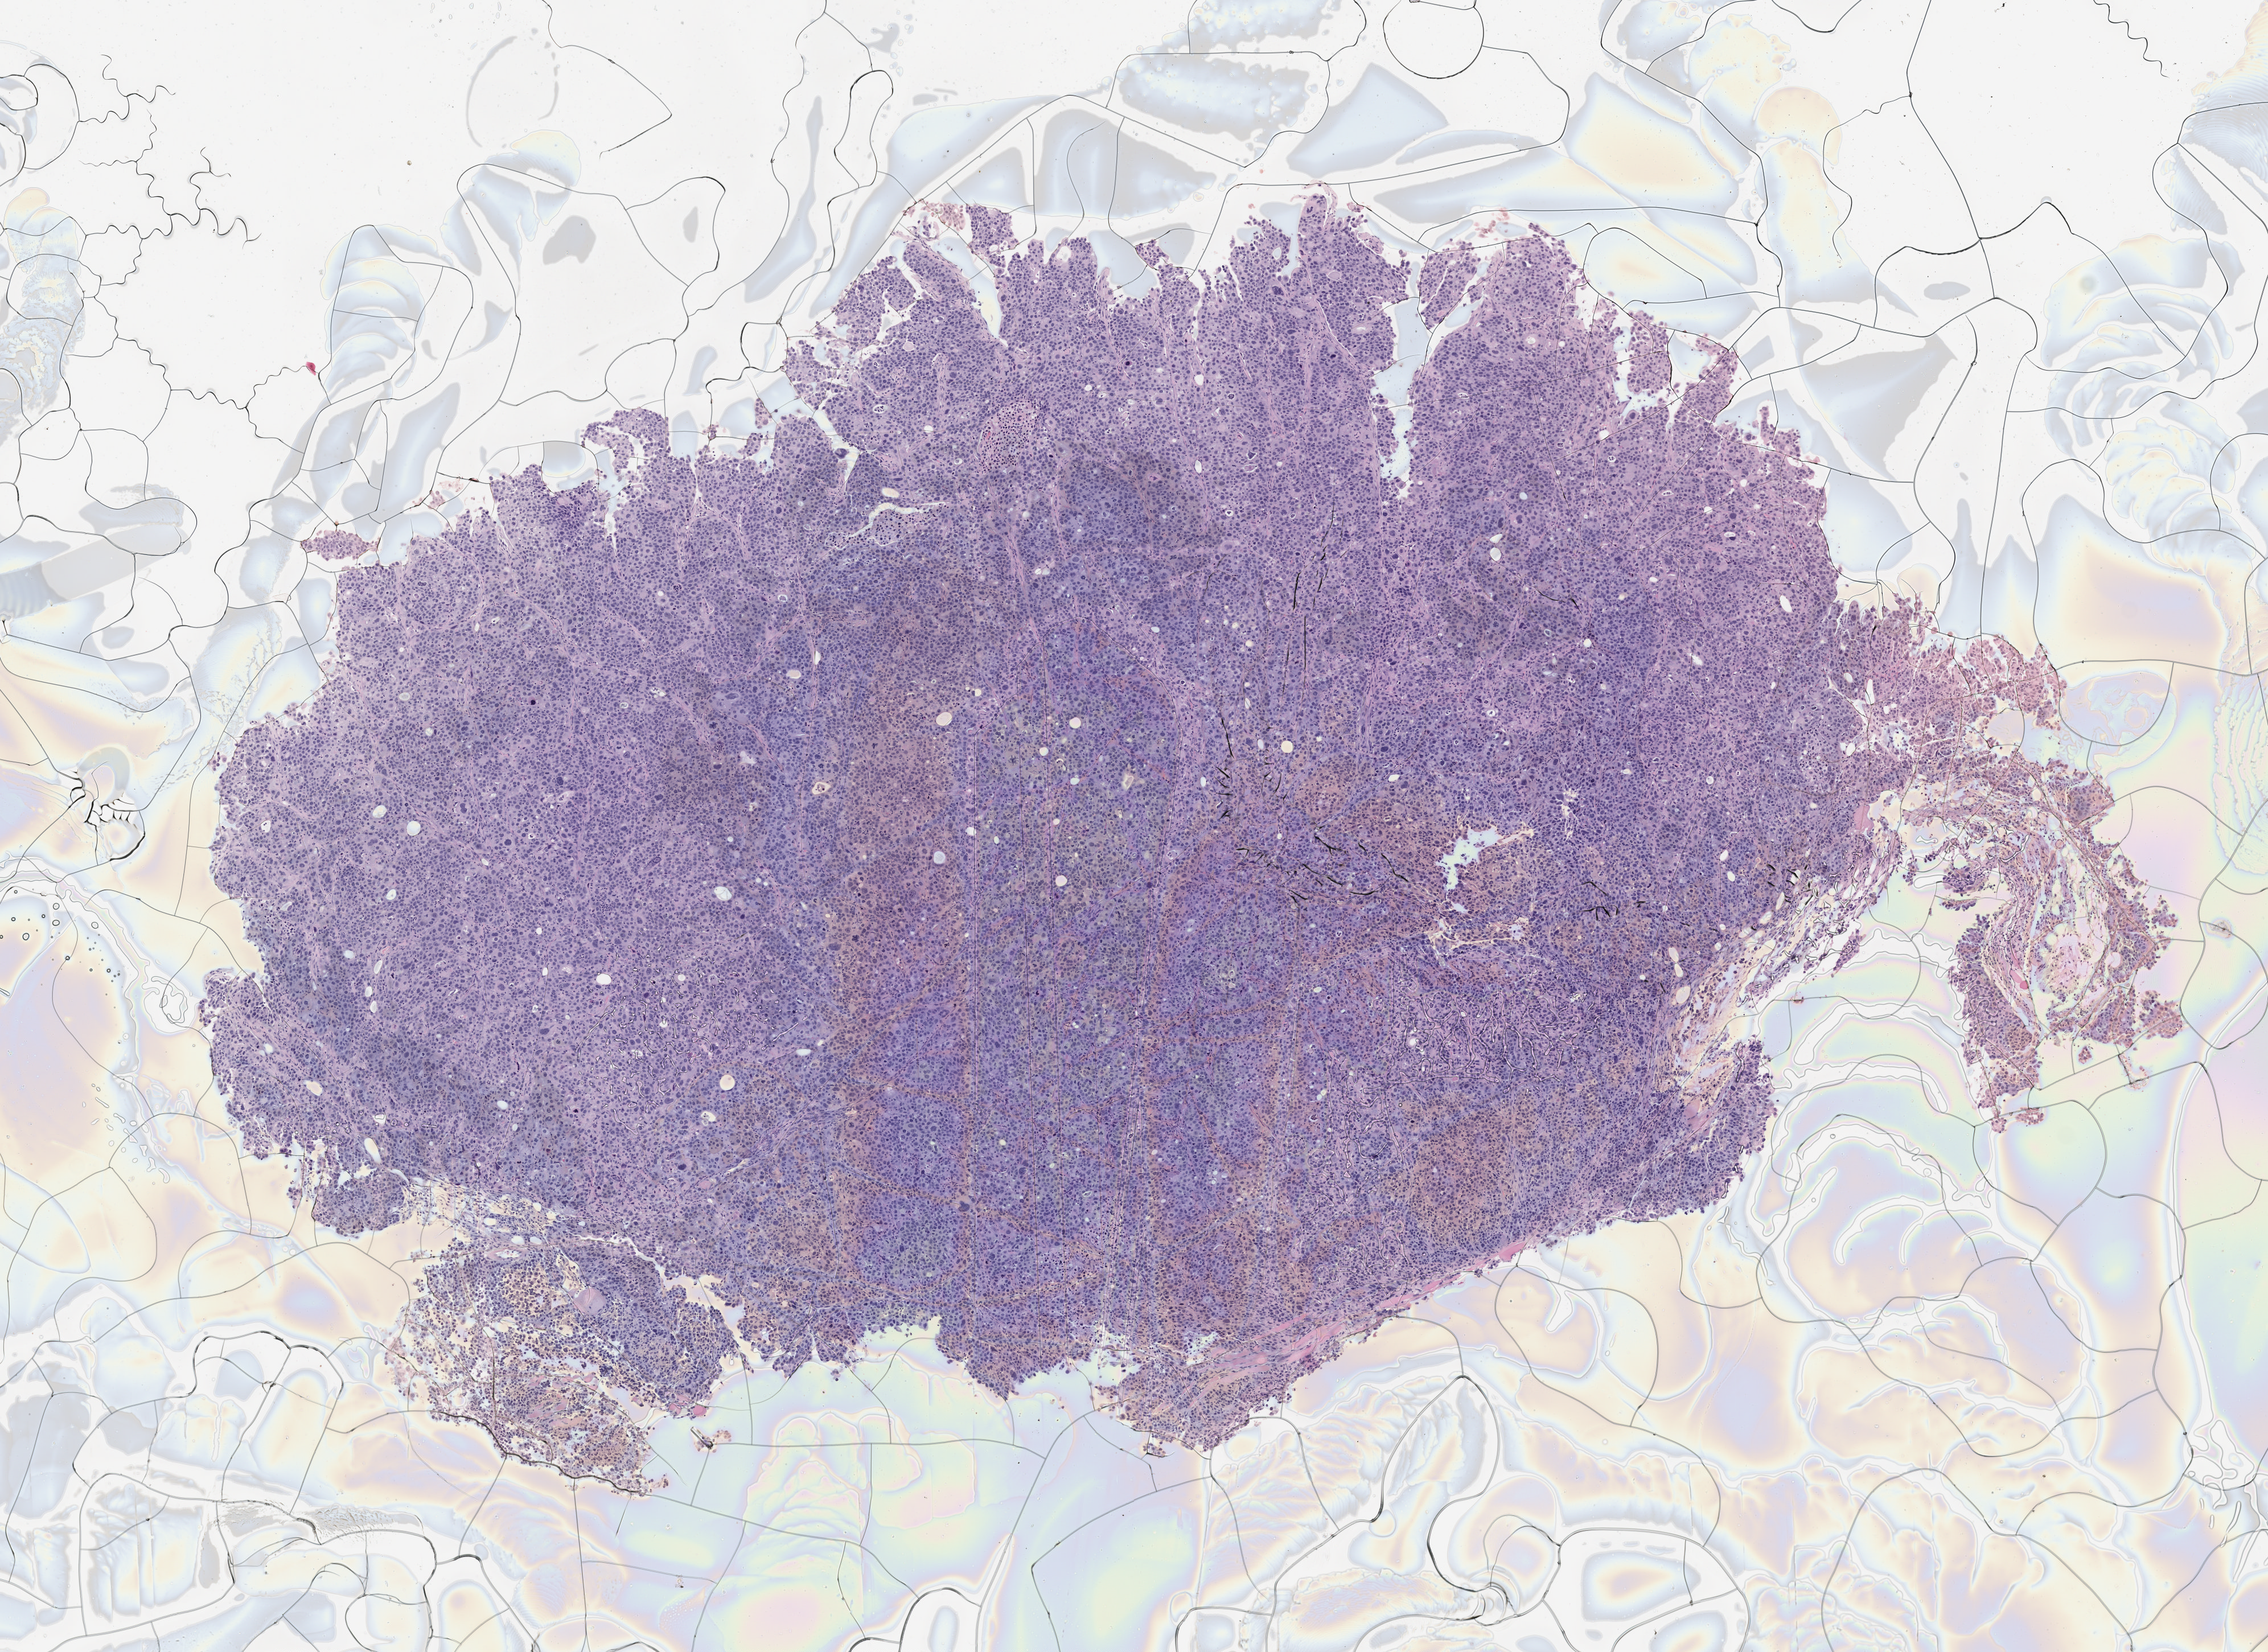
Whole-slide image, H&E: patient-derived xenograft (human tumor grown in a mouse), passage 3 — shown as a low-resolution overview of the whole scanned area (about 8.0 x 5.8 mm). FFPE section. Tumor site category: bladder.
Originating patient diagnosis: Urothelial Carcinoma.